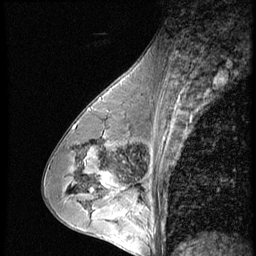
Breast MRI (dynamic contrast-enhanced), one sagittal slice; position 31 of 56 along the scan axis; 3 images stored at this slice position (order not interpretable as contrast timing); 1.5 T; TE 4.2 ms, TR 9 ms; 2.5 mm slice thickness; 256 × 256 image matrix, field of view 180 × 180 mm. Patient: female, 43 years. From the clinical record (not read from this slice): setting: breast cancer imaged before/during neoadjuvant chemotherapy; receptor status: HR-positive, HER2-negative.
Outlined on this slice (semi-automatically segmented with operator editing):
- analysis volume of interest (the breast-tissue region the enhancement analysis was run in; not a lesion): bounding box <120,160,163,207> (left, top, right, bottom; pixels)
- tumour enhancement mask (voxels above the 140 % enhancement threshold inside the analysis volume of interest): <120,190,125,193>